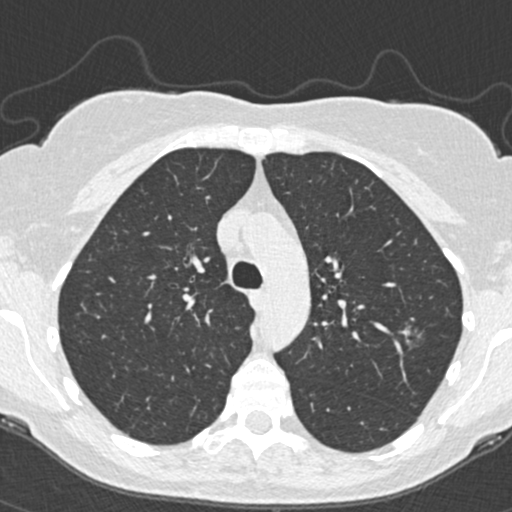
Low-dose screening chest CT, one axial slice. Reconstruction kernel B30f. 120 kVp. Lung window (W 1500 / L -600 HU). 1 mm slice thickness. 512 × 512 image matrix, field of view 298 × 298 mm.
Outlined on this slice (outlined manually by an expert reader):
- lesion 1 (tumor, upper lobe of left lung): box from (x=400, y=326) to (x=414, y=339) px